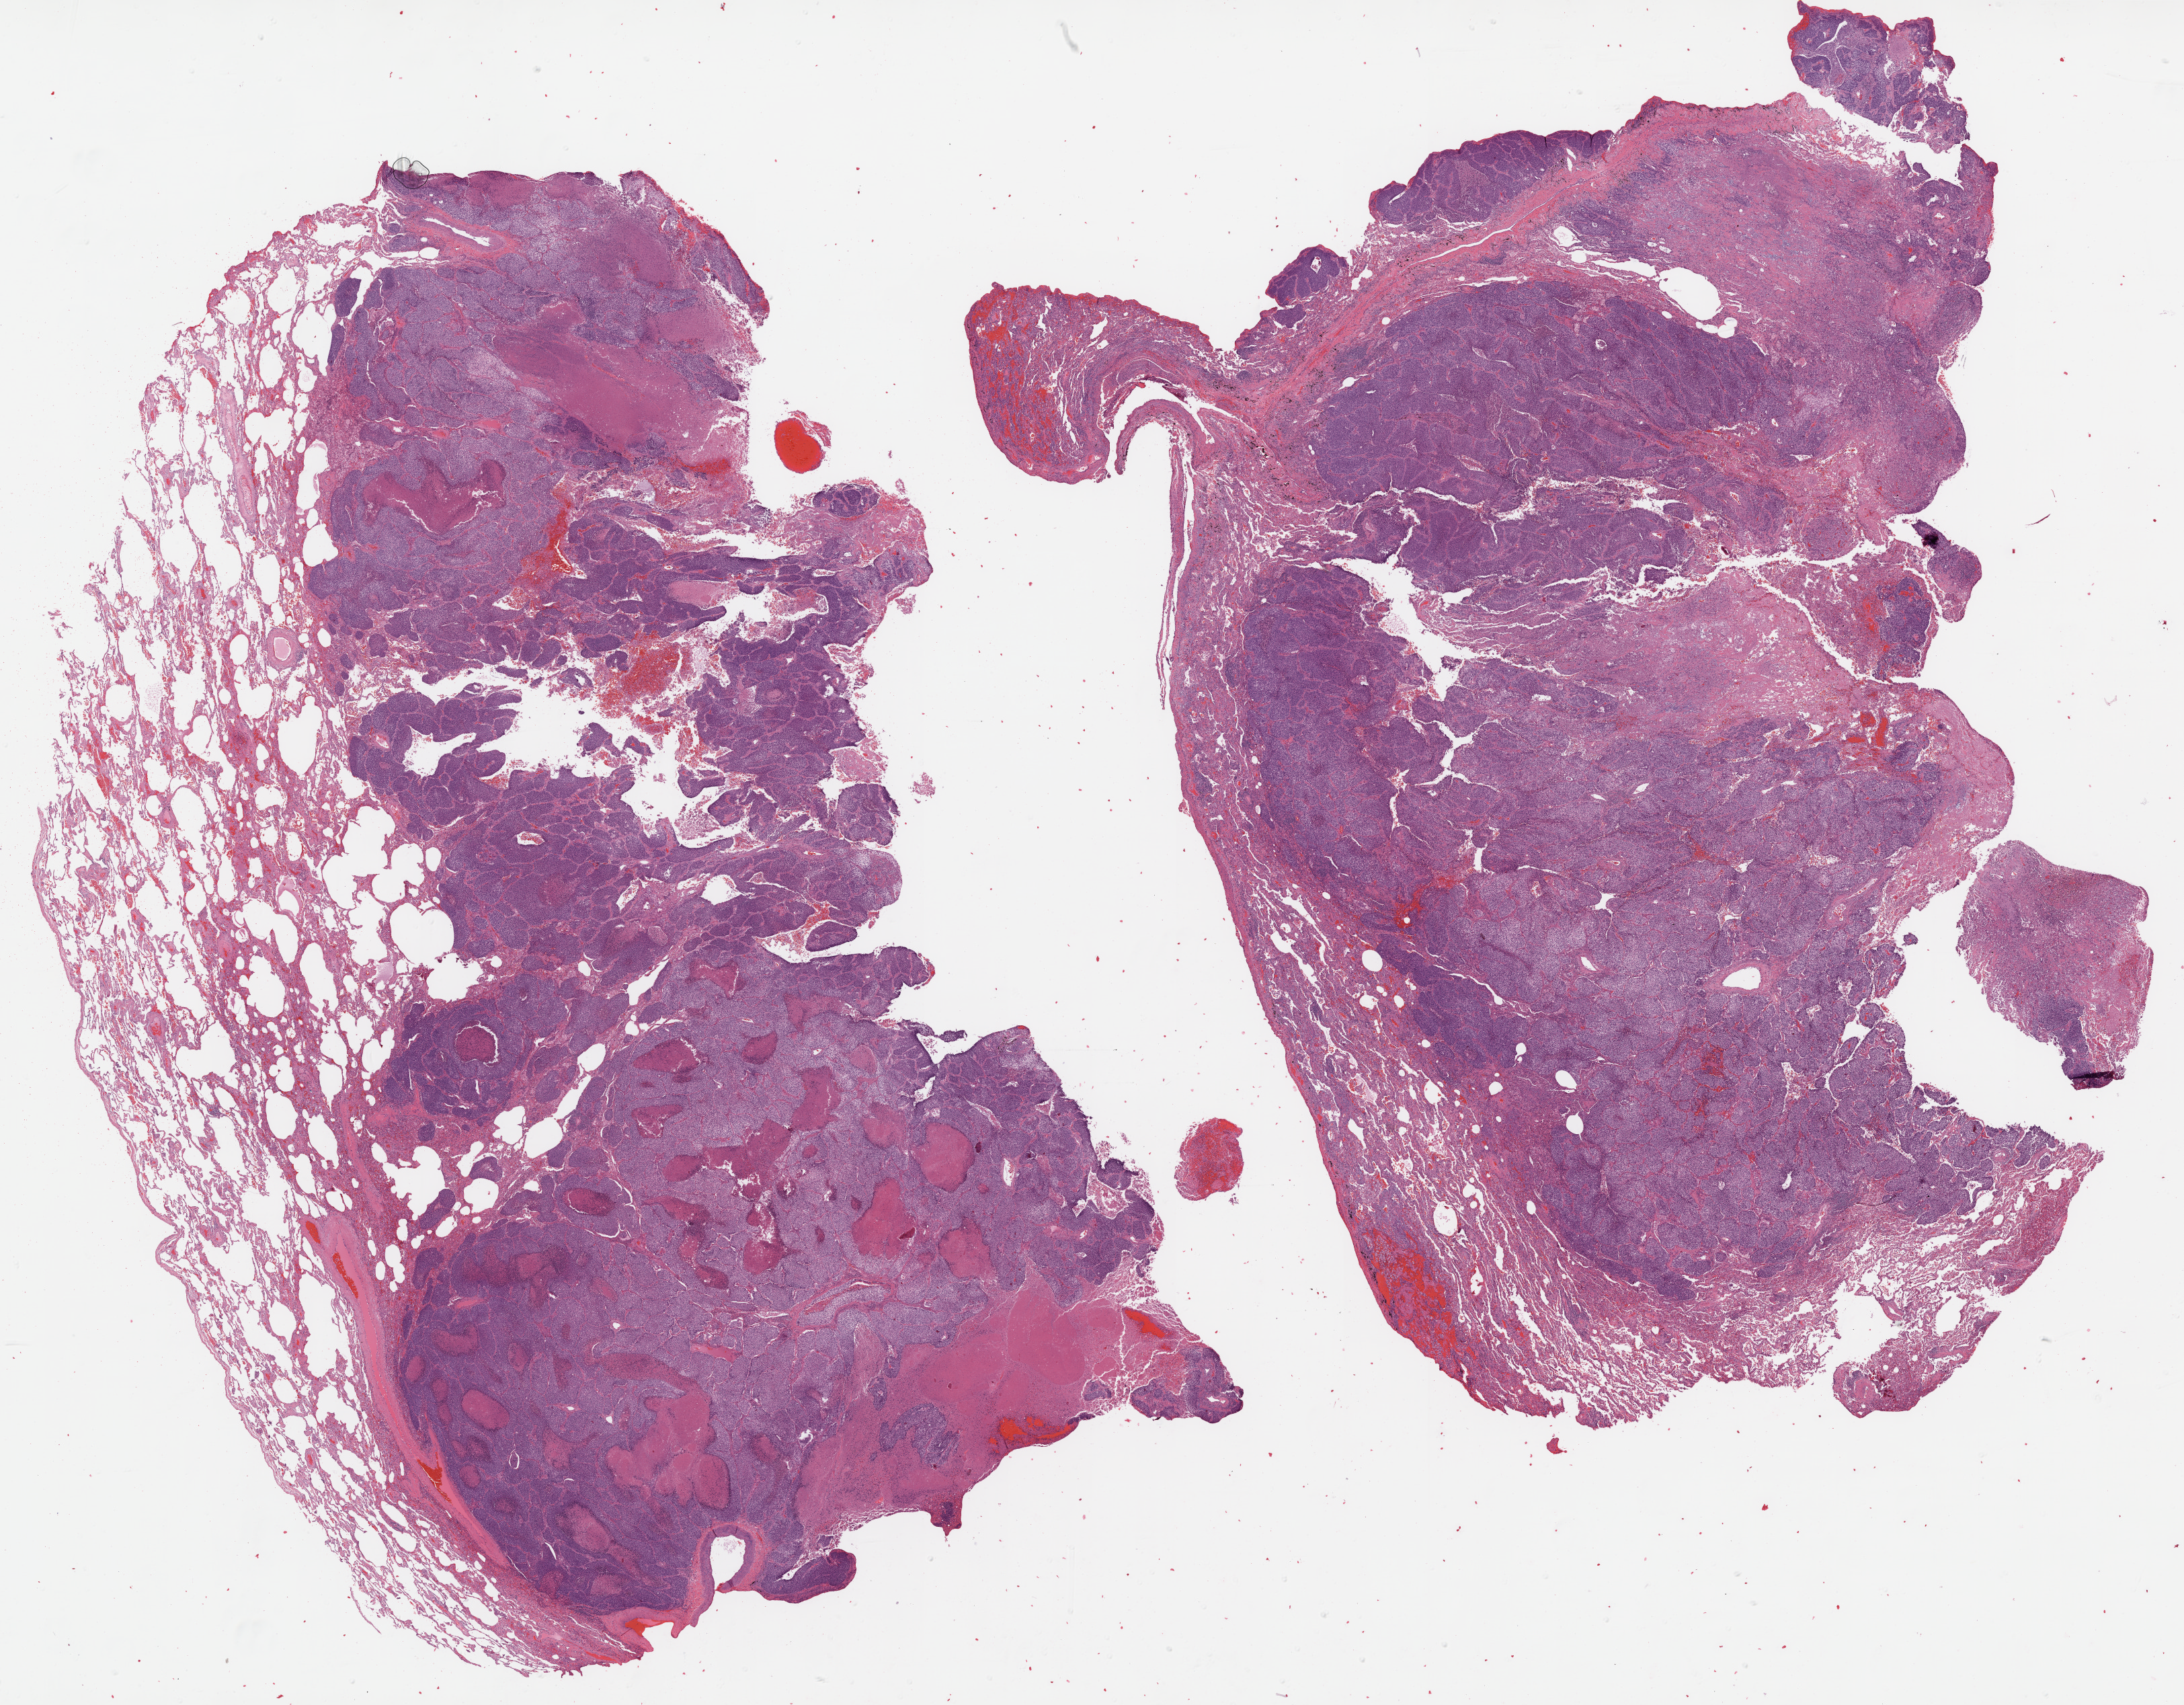
Whole-slide histology image, H&E, low-resolution overview of the scanned area, about 26.1 x 20.4 mm (from a 20x scan). FFPE section. Sample: primary tumour, lung. Female, age 83 years at initial diagnosis.
TNM: T1 N0 M0. AJCC pathologic stage: IB. Diagnosis: Squamous cell carcinoma, NOS.